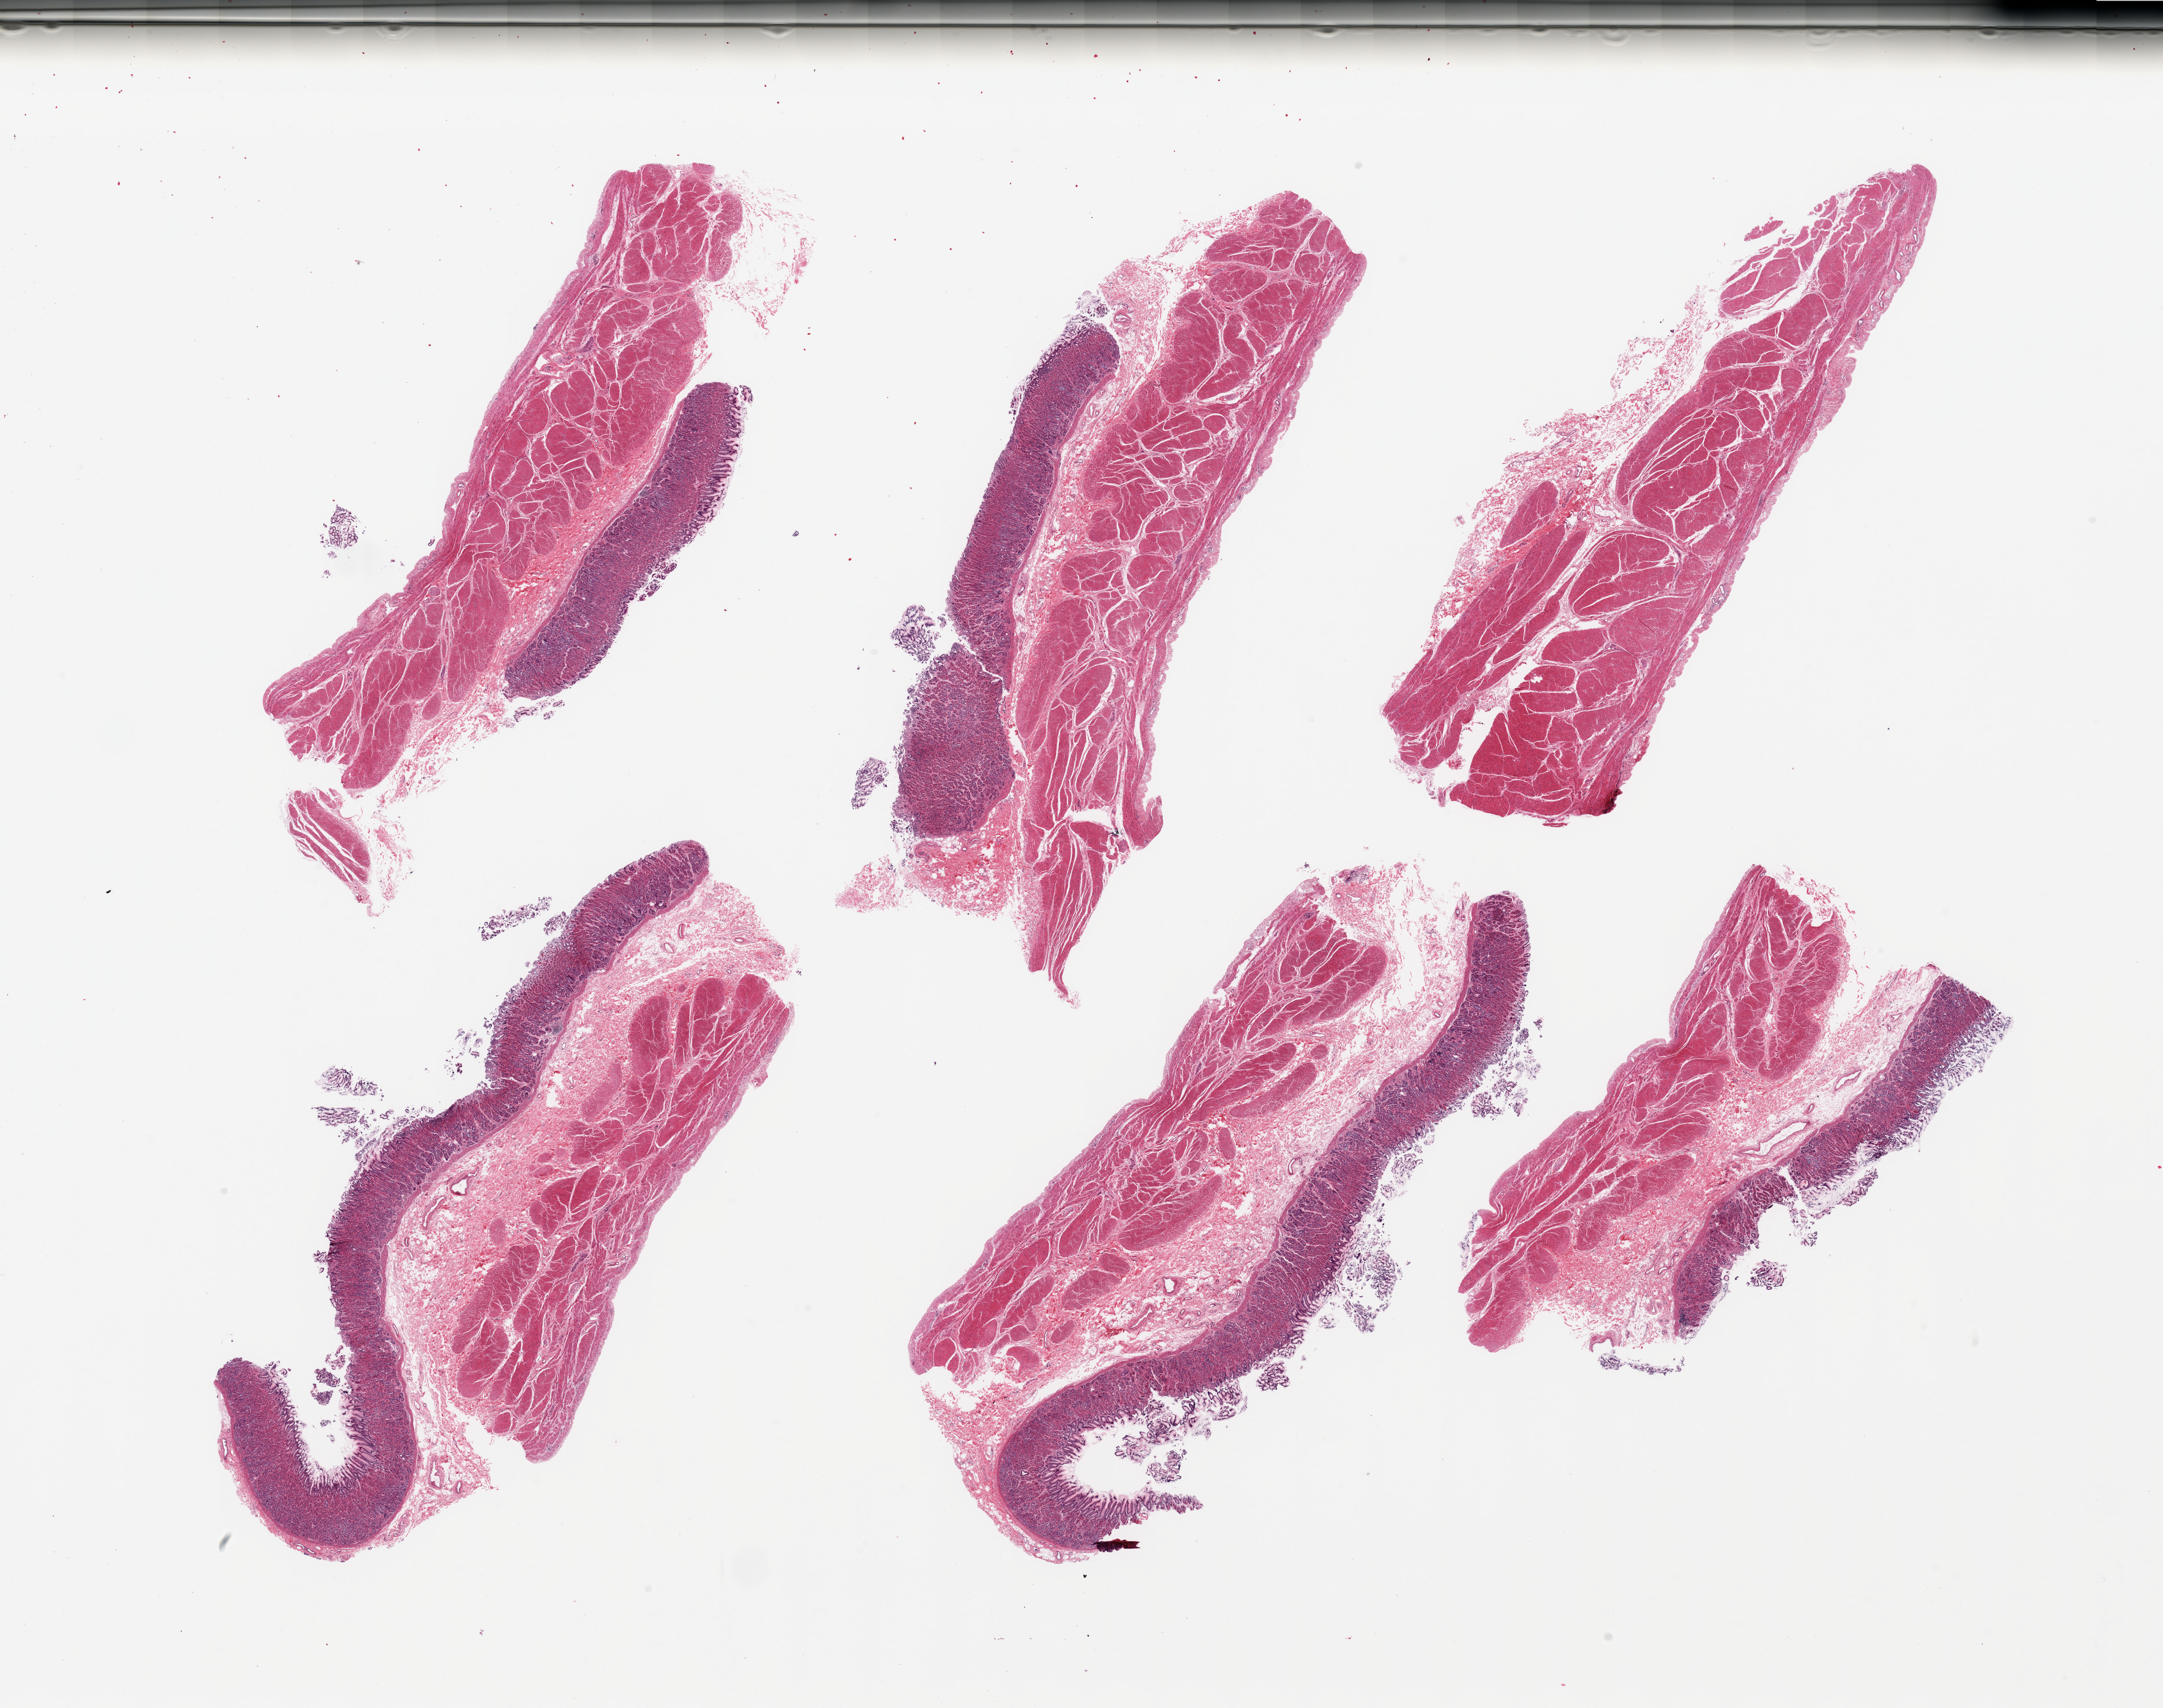
Digitized H&E-stained section, a low-resolution overview of the entire scanned area, about 29.5 x 23.3 mm (acquisition: 20x scan). PAXgene-fixed paraffin-embedded (PFPE) section. Sampled site (target tissue): stomach. Donor tissue sample. Donor sex: female.
Review note (as recorded): 6 pieces, well-preserved target mucosa up to ~1mm, ~20% thickness.